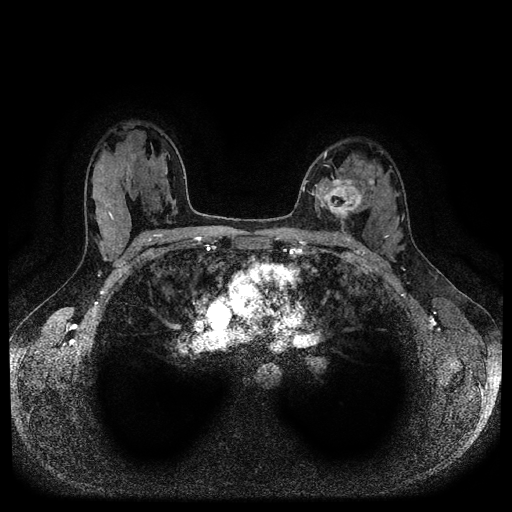
Breast MRI (dynamic contrast-enhanced, multi-phase), one axial slice. Position 64 of 116 along the scan axis. Dynamic contrast-enhanced series, time point 2 of 5 at this slice position (early post-contrast). 1.5 T. TE 2.6 ms, TR 5.3 ms. 512 × 512 image matrix, field of view 350 × 350 mm. Patient: female, 33 years.
Annotated regions visible in this slice (semi-automatically segmented with operator editing):
- breast lesion (labelled 'tumour' in the annotation; benign lesions carry a separate 'benign' label): bounding box [x1, y1, x2, y2] px = [317, 177, 366, 224]